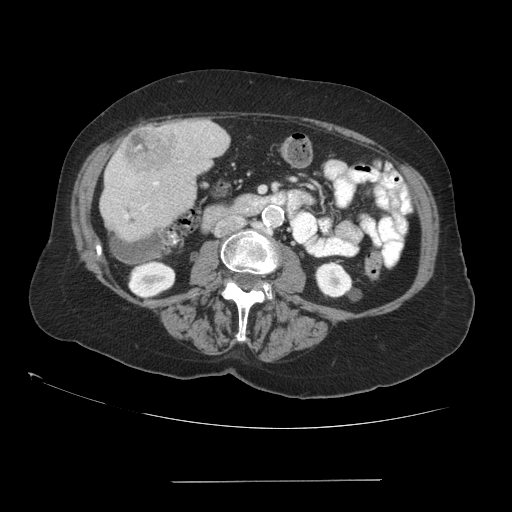
Contrast-enhanced abdominal CT (liver protocol), one axial slice; position 26 of 89 along the scan axis; 140 kVp; soft-tissue window (W 400 / L 40 HU); 2.5 mm slice thickness; 512 × 512 image matrix, field of view 400 × 400 mm. Case-level facts recorded for this patient, not image findings: diagnosis: hepatocellular carcinoma (patient treated with transarterial chemoembolisation; whether this scan precedes or follows treatment is not stated here); TNM stage (as recorded): Stage-IVA.
Outlined on this slice (semi-automatically segmented with operator editing):
- liver parenchyma outside the tumour (the mass and vessels are separate outlines, so this box may not span the whole liver): bounding box (x1, y1, x2, y2) in pixels: (100, 120, 228, 242)
- mass: (124, 129, 177, 174)
- liver vessels: (125, 182, 158, 218)